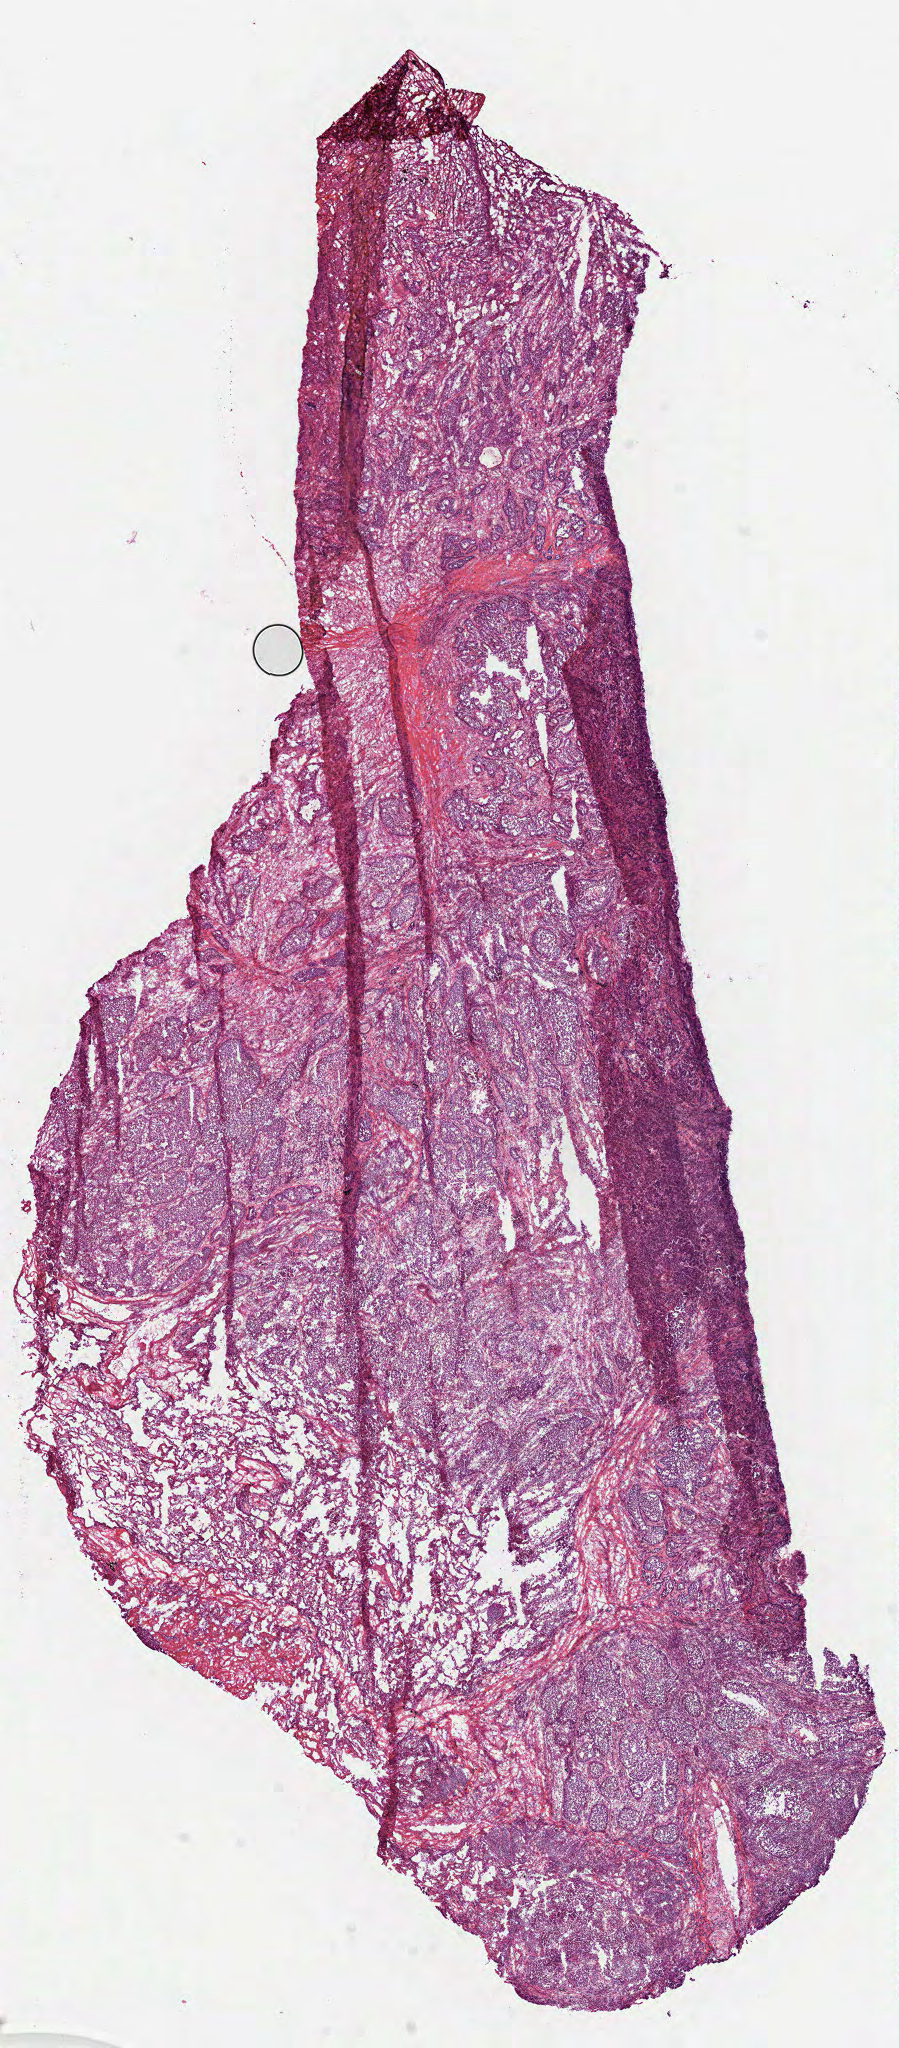
Whole-slide histology image, H&E, whole scanned area (about 7.3 x 16.5 mm) shown as a low-resolution overview. Frozen section from the bottom of the tissue portion. Lung, primary tumour sample. Male patient; age at initial diagnosis 66 years. Pathologist review of this section (percent, as recorded): tumour cells 65%, tumour nuclei 65%, normal cells 10%, stromal cells 23%, necrosis 2%. Infiltration values recorded for this section: lymphocyte infiltration 8%.
- TNM: T2 N0 M1
- AJCC pathologic stage: IV (7th edition)
- diagnosis: Adenocarcinoma, NOS